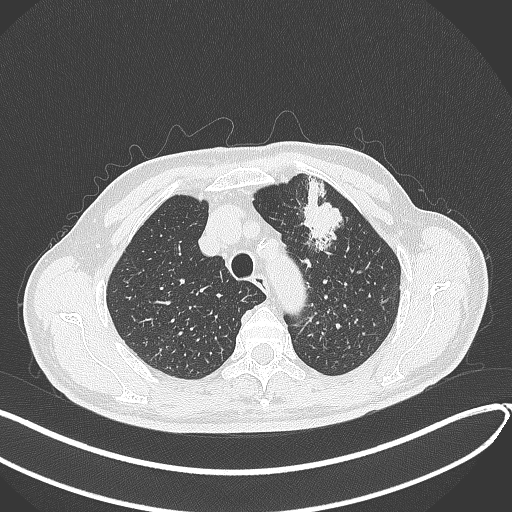
Chest CT, one axial slice; slice 336 of 459 in the series (ordered by position); reconstruction kernel B70f; 120 kVp; lung window (W 1500 / L -600 HU); 1 mm slice thickness; 512 × 512 image matrix, field of view 400 × 400 mm. Patient: male, 74 years. From the clinical record (not read from this slice): clinical TNM (as recorded): T2b N0 M1c.
Structures marked on this image (bounding box drawn by a radiologist):
- lung tumour (recorded histology: adenocarcinoma): bounding box [x1, y1, x2, y2] px = [296, 174, 349, 254]